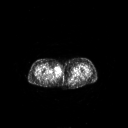
FDG PET of an extremity soft-tissue mass (from a PET/CT study), one axial slice; slice 232 of 311 in the series (ordered by position); 3.27 mm slice thickness; 128 × 128 image matrix. Female patient, age 78 years. From the clinical record (not read from this slice): histological type: leiomyosarcoma; grade: intermediate; site of the primary tumour: parascapusular.
Outlined on this slice (expert contour drawn on MRI and transferred to this co-registered scan by the dataset authors):
- gross tumour volume including surrounding oedema: box from (x=54, y=66) to (x=62, y=76) px
- gross tumour volume (mass): (x=54, y=66)–(x=62, y=76)